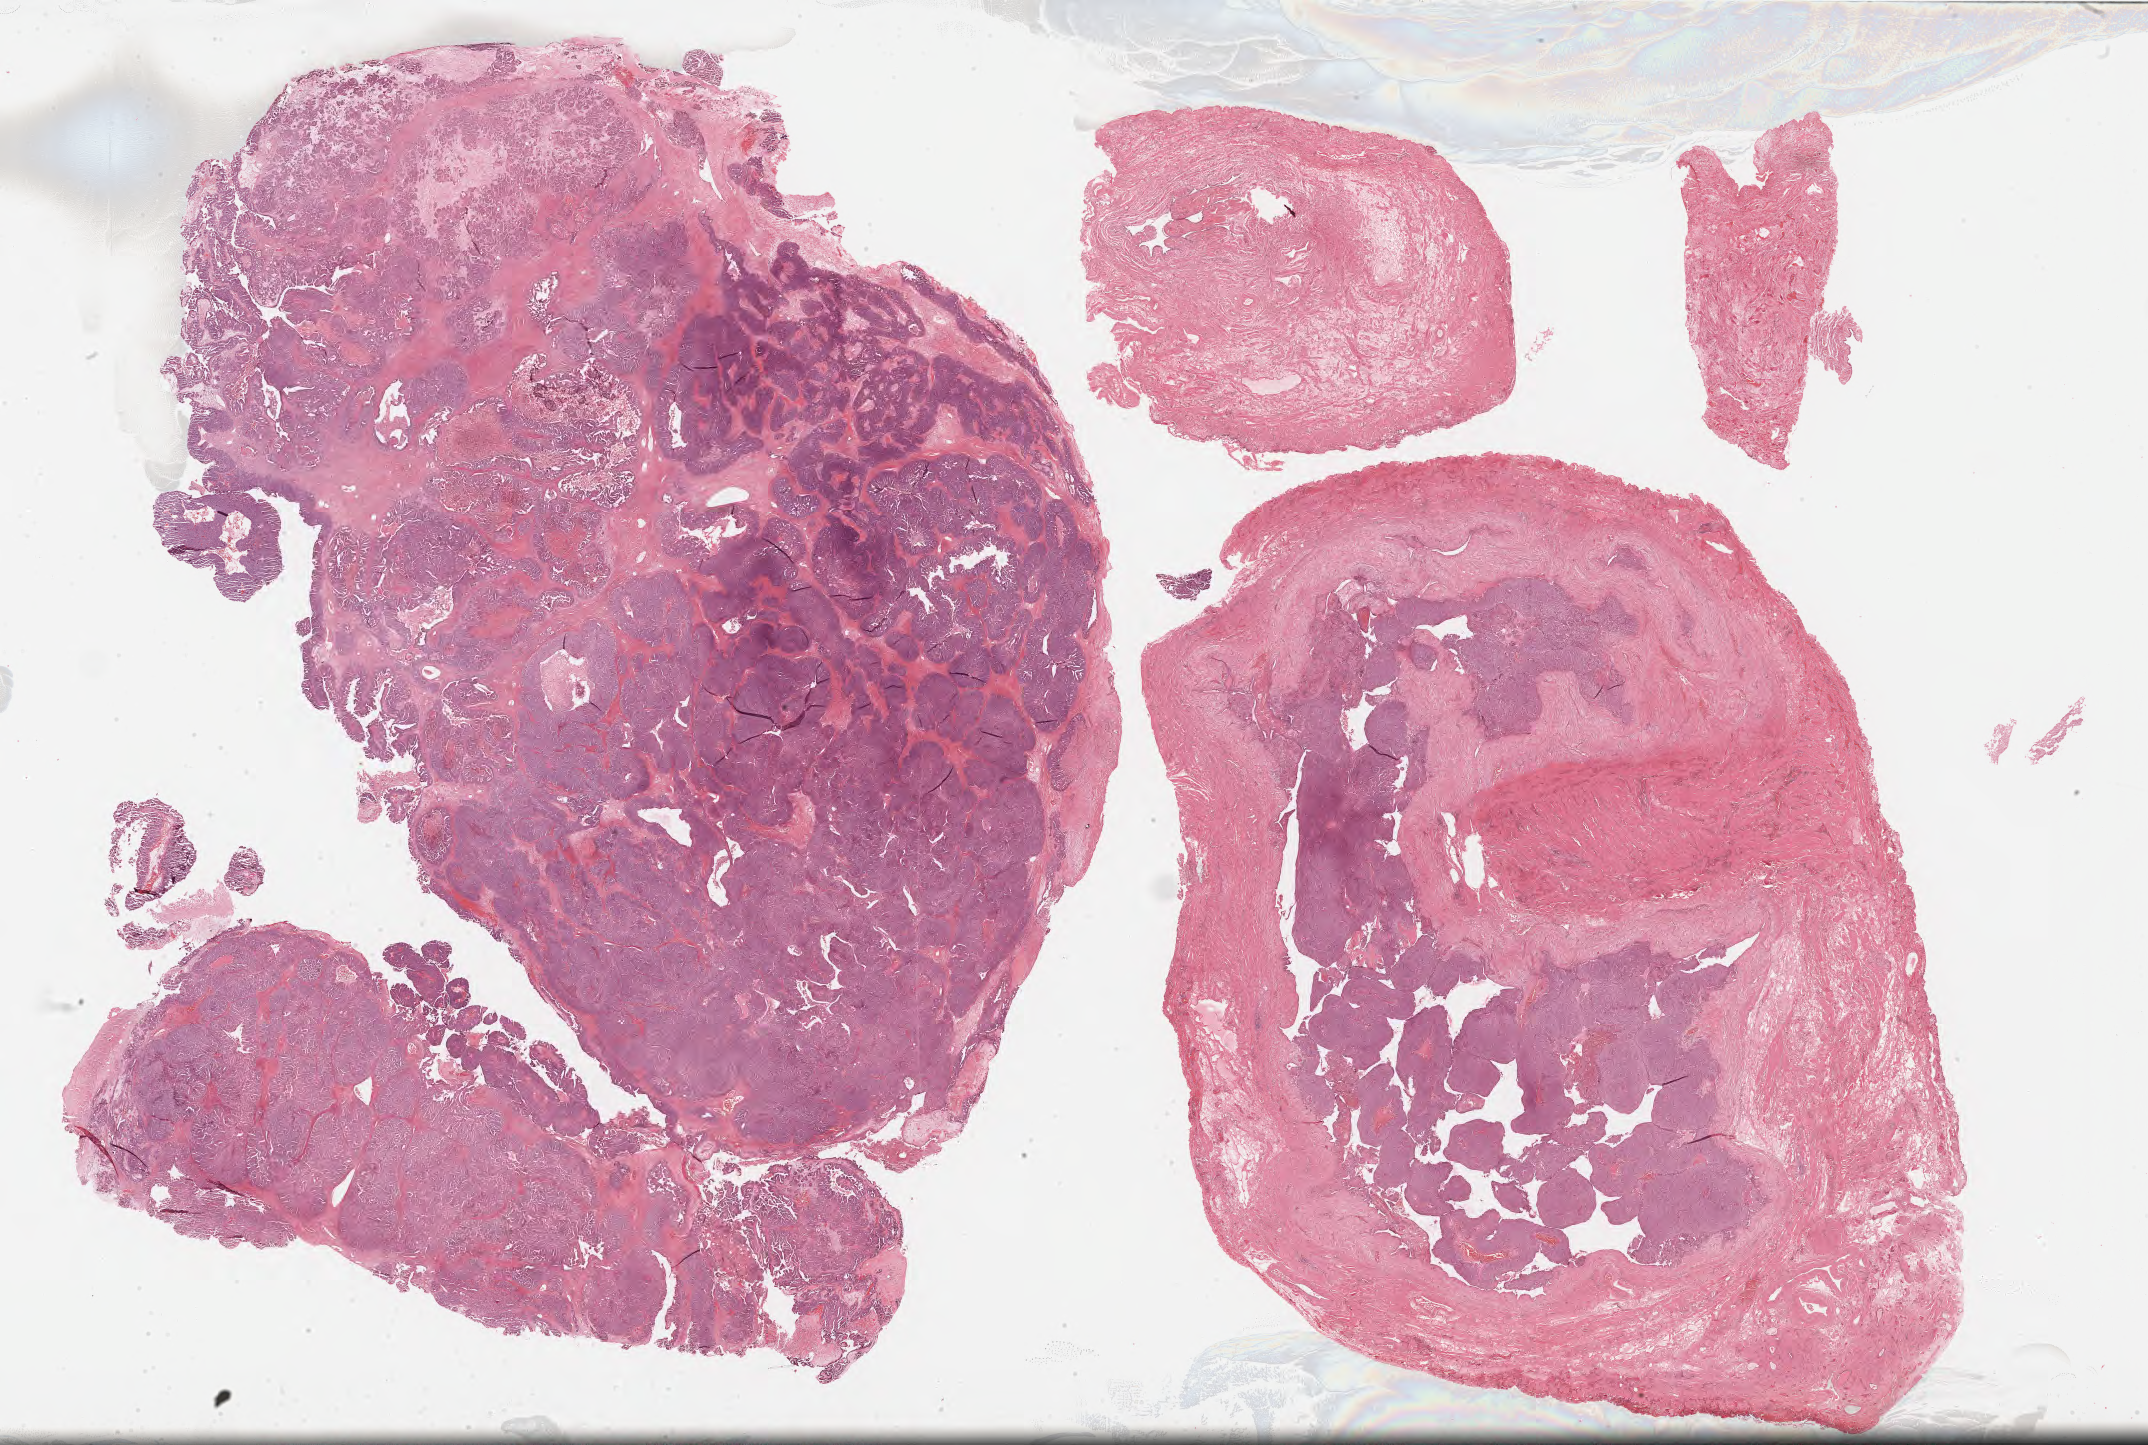
Digitized Hematoxylin and eosin (H&E) stained tissue section (whole slide) — a low-resolution overview of the entire scanned area, about 34.7 x 23.3 mm, formalin-fixed paraffin-embedded (FFPE) diagnostic section, ovary, primary tumour sample. Patient: female, age at initial diagnosis 57 years. Histologic grade: G3 (poorly differentiated).
Histologic diagnosis: Serous cystadenocarcinoma, NOS. FIGO stage: IIIC.